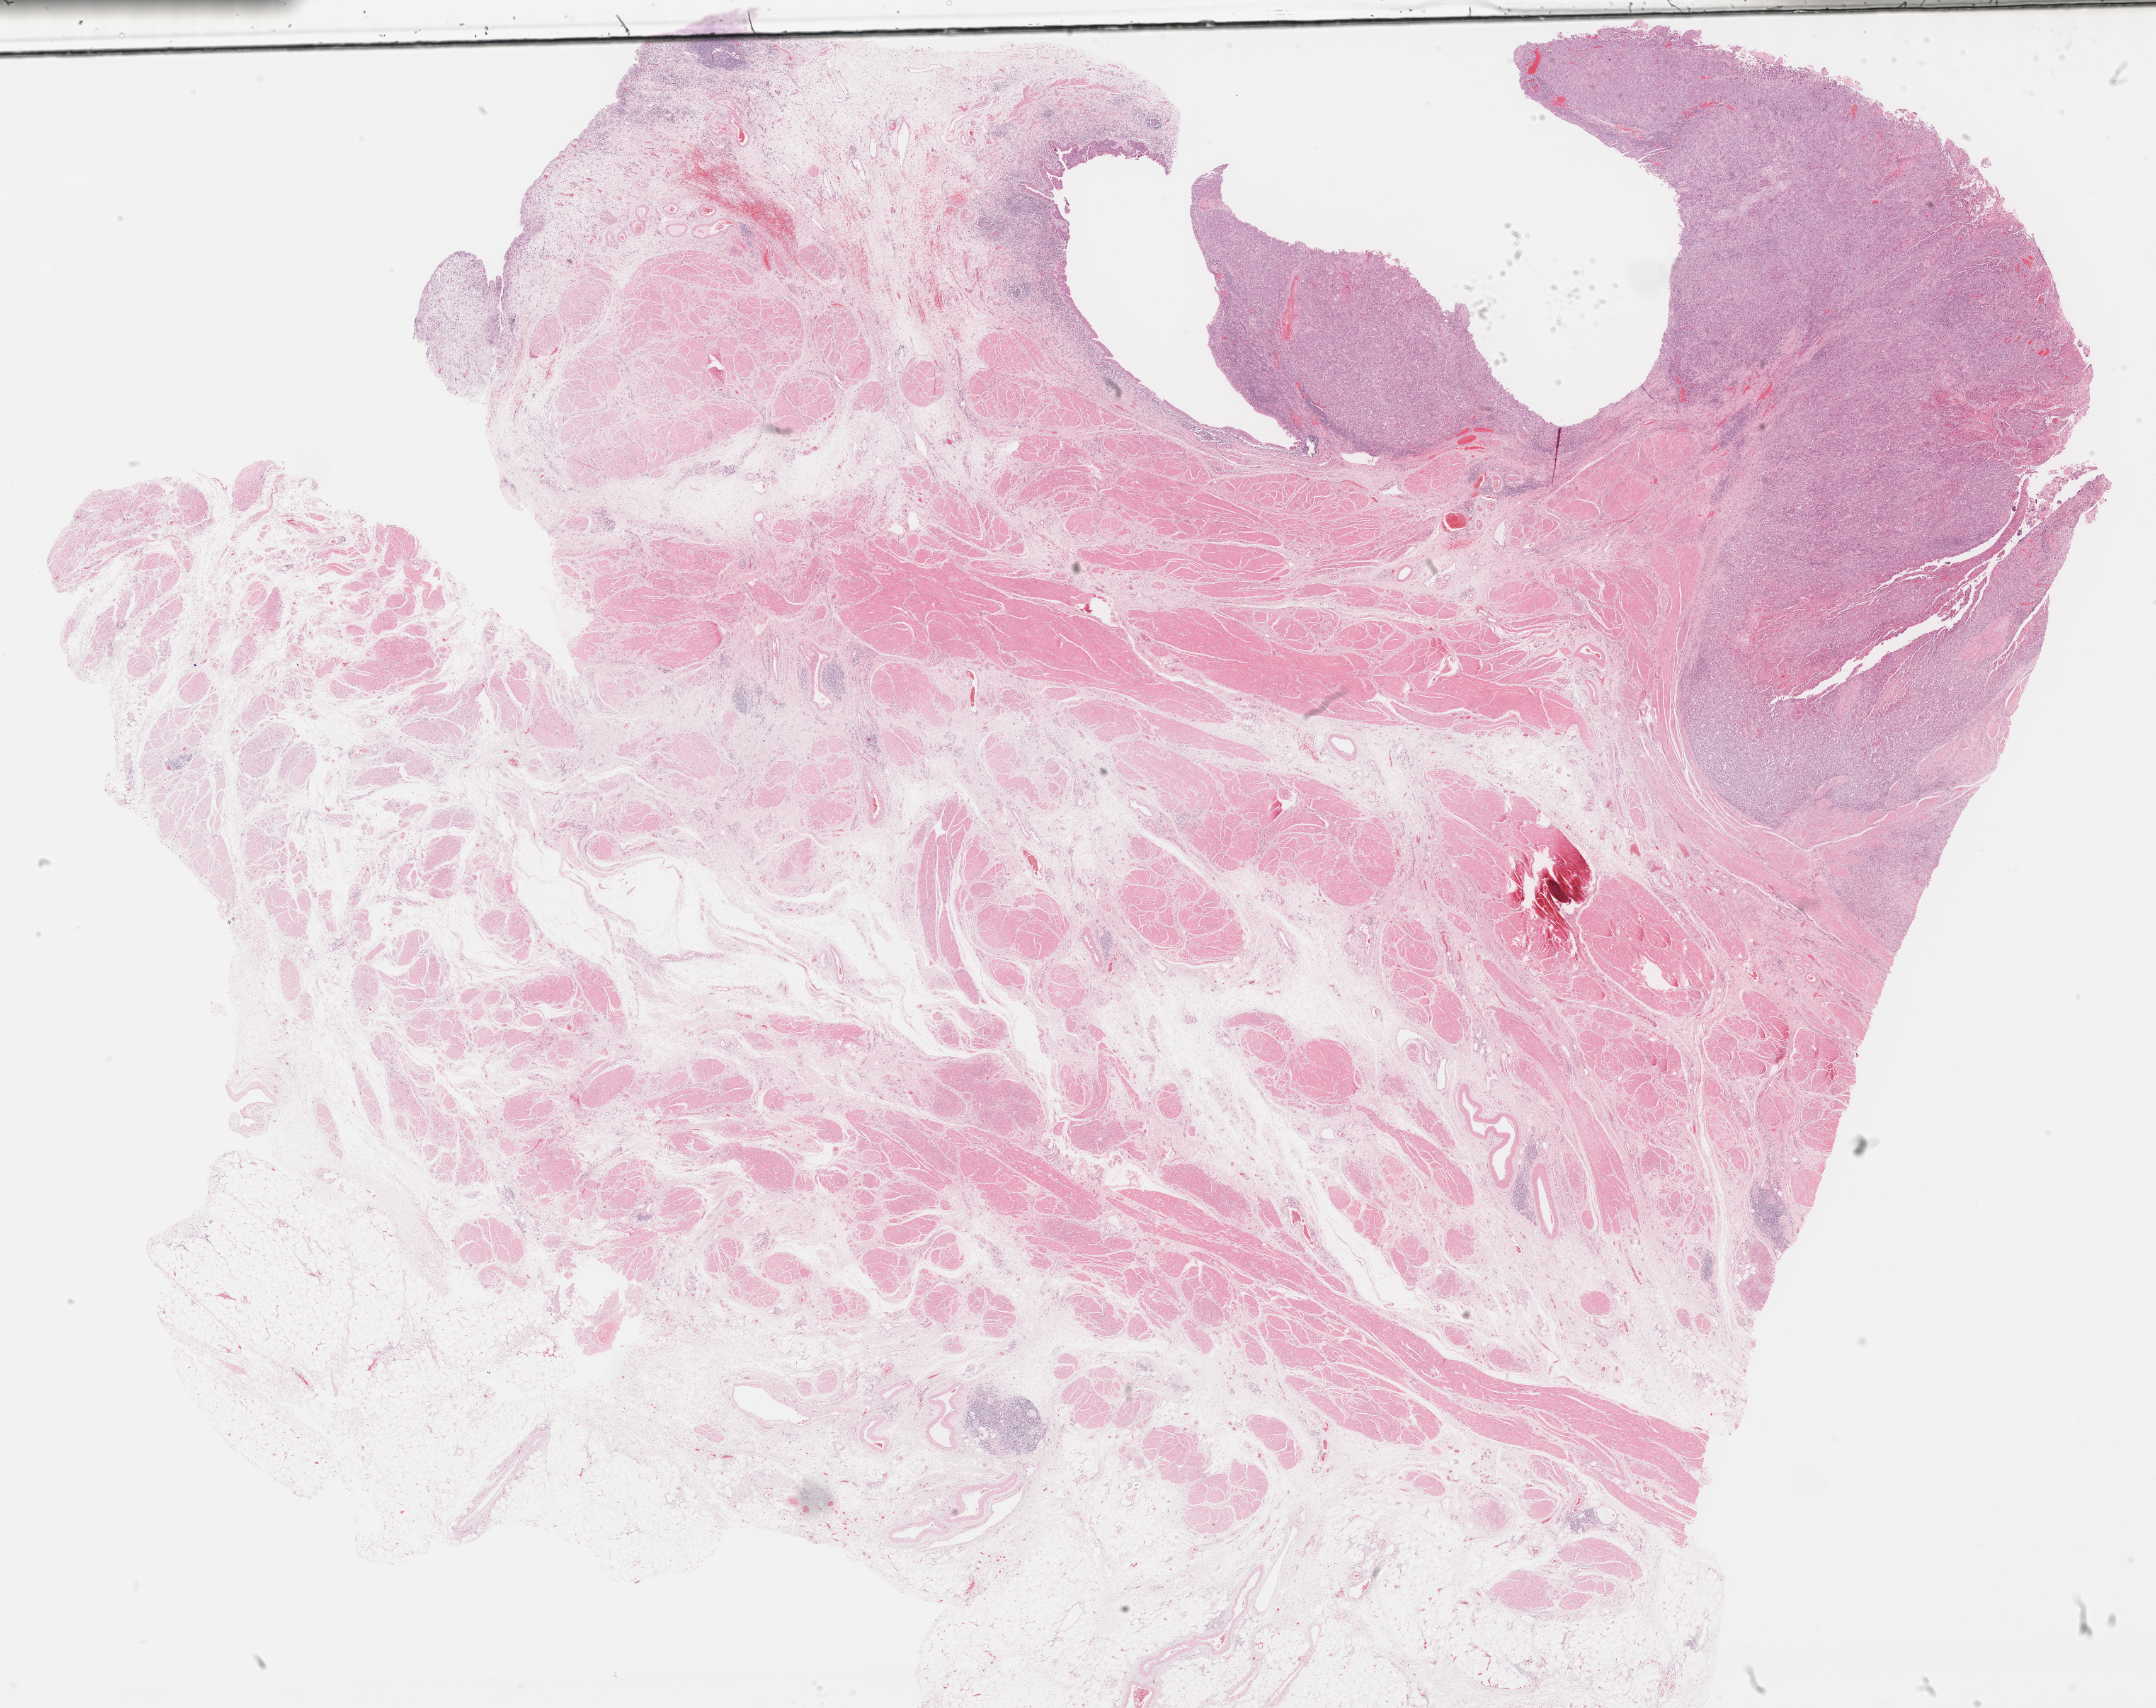
Whole-slide histology image, Hematoxylin and eosin (H&E) stained — low-resolution overview of the scanned area, about 27.7 x 21.9 mm (acquisition: 40x scan); formalin-fixed paraffin-embedded (FFPE) diagnostic section; primary tumour sample from the bladder. Female patient; age at initial diagnosis 75 years. Histologic grade: high grade.
AJCC pathologic stage: IV. Histologic diagnosis: Transitional cell carcinoma (posterior wall of bladder).